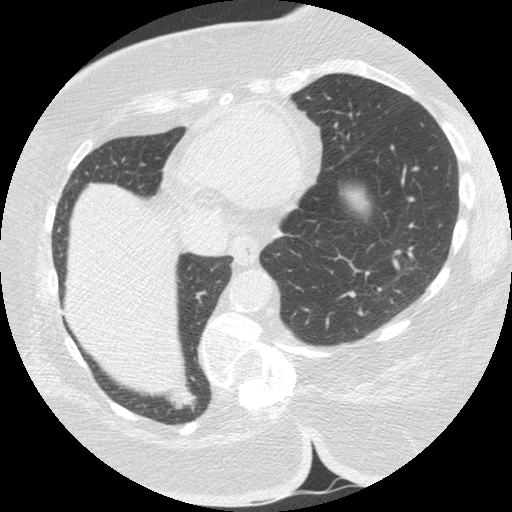
Low-dose screening chest CT, one axial slice. Slice 47 of 151 in the series (ordered by position). Reconstruction kernel STANDARD. Lung window (W 1500 / L -600 HU). 2.5 mm slice thickness. 512 × 512 image matrix, field of view 340 × 340 mm.
Outlined on this slice (expert manual segmentation):
- lesion 1 (tumor, lower lobe of right lung): box from (x=168, y=381) to (x=197, y=411) px